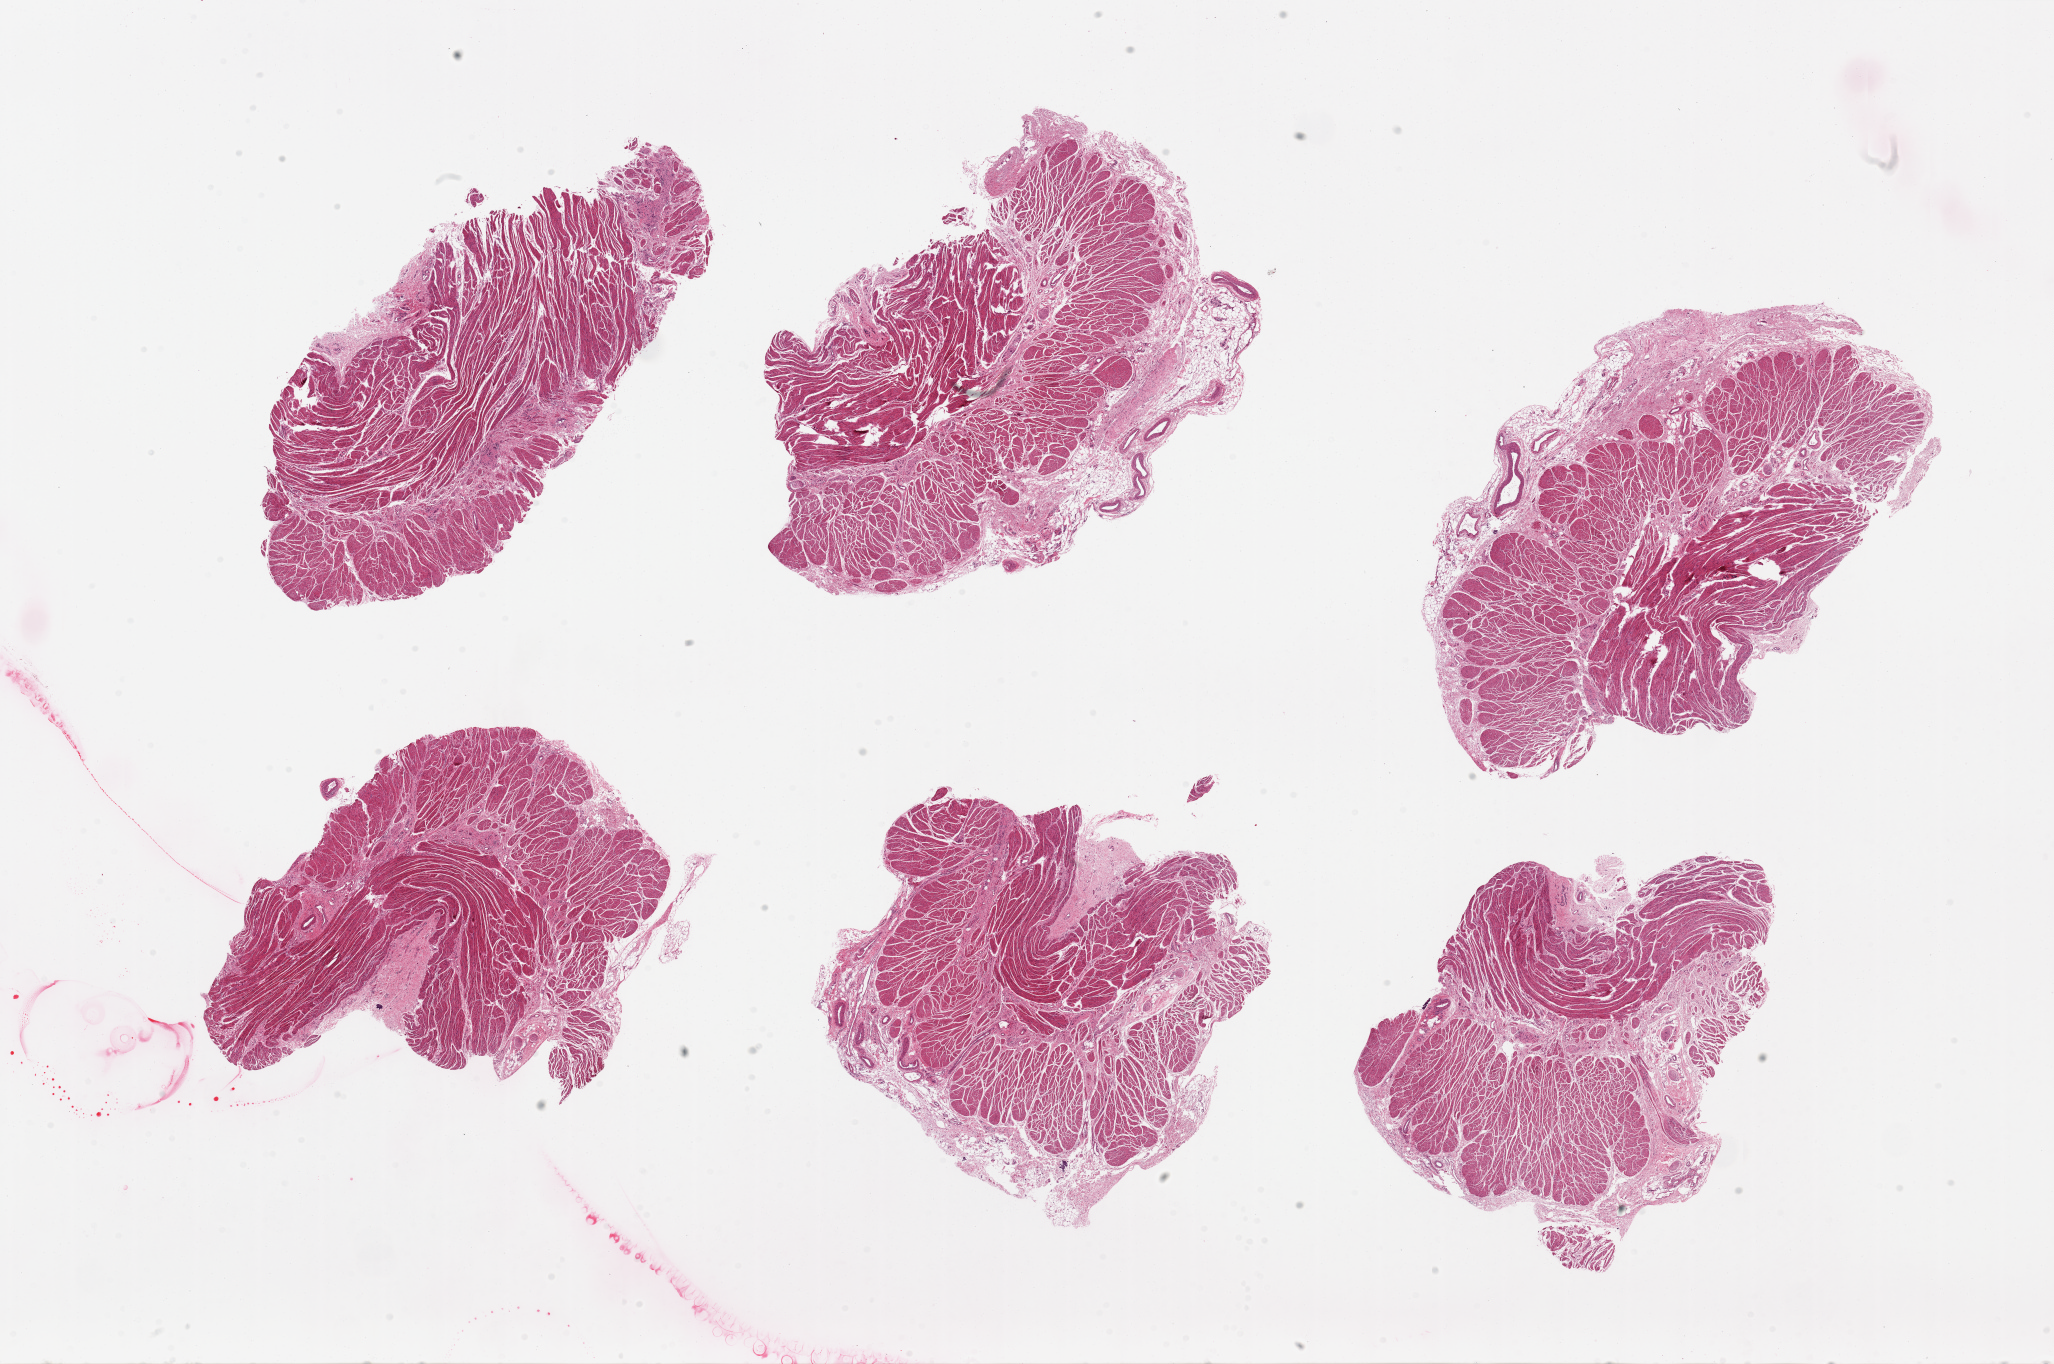
Hematoxylin and eosin (H&E) whole-slide image, brightfield, a low-resolution overview of the entire scanned area, about 32.5 x 21.6 mm (acquisition: 20x scan), PAXgene-fixed, paraffin-embedded tissue, sampled site (target tissue): gastroesophageal junction, tissue donor sample. Donor sex: male.
Reviewer comment on this tissue sample: 6 pieces, up to 9.5x5mm; all muscularis, good specimens.